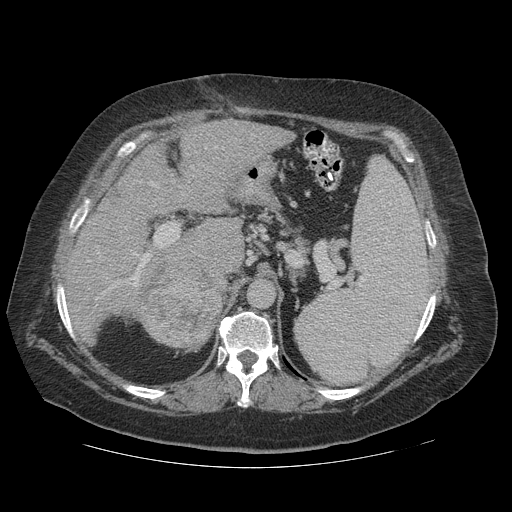
Contrast-enhanced abdominal CT (liver protocol), one axial slice; position 75 of 121 along the scan axis; reconstruction kernel STANDARD; soft-tissue window (W 400 / L 40 HU); 2.5 mm slice thickness; 512 × 512 image matrix, field of view 420 × 420 mm. Case-level facts recorded for this patient, not image findings: diagnosis: hepatocellular carcinoma (patient treated with transarterial chemoembolisation; whether this scan precedes or follows treatment is not stated here); TNM stage (as recorded): Stage-IIIA; Child-Pugh class: A; tumour differentiation: well differentiated; tumour nodularity: multinodular.
Annotated regions visible in this slice (semi-automatically segmented with operator editing):
- liver parenchyma outside the tumour (the mass and vessels are separate outlines, so this box may not span the whole liver): bounding box (x1, y1, x2, y2) in pixels: (66, 120, 294, 326)
- mass: (133, 258, 224, 353)
- liver vessels: (87, 134, 255, 299)